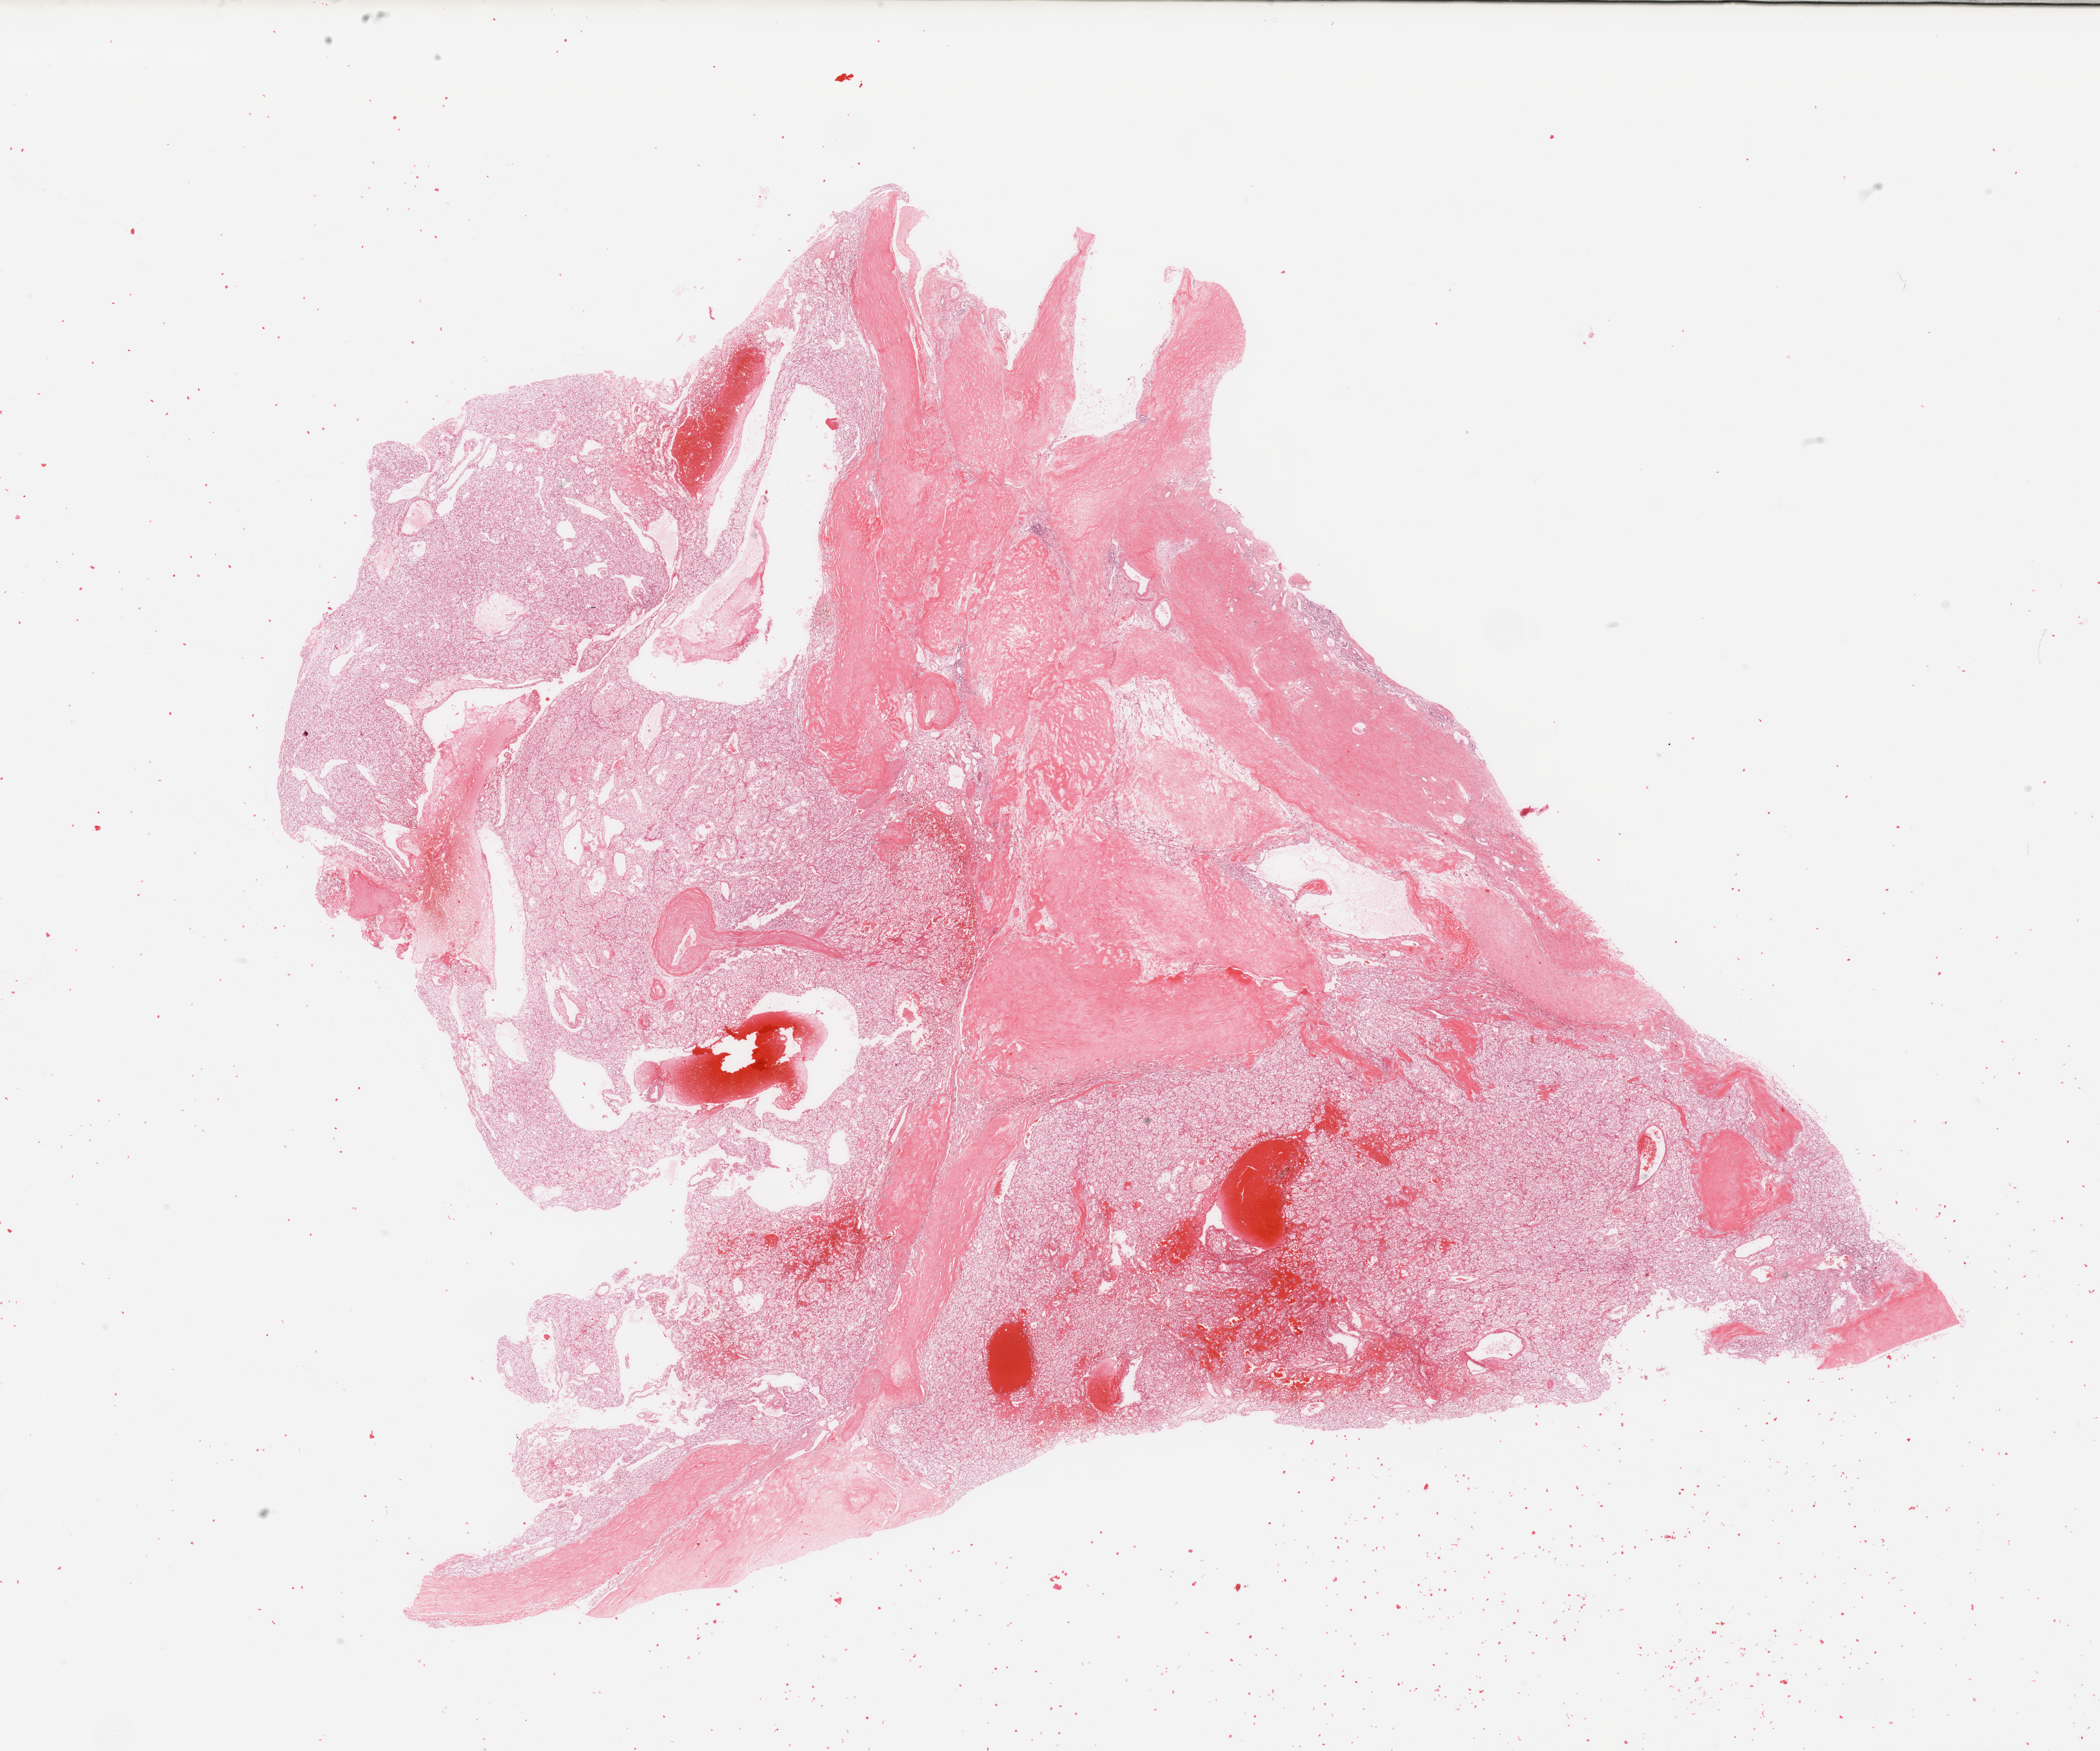
Whole-slide histology image, H&E-stained — a low-resolution overview of the entire scanned area, about 25.6 x 21.3 mm; tumour tissue sample, sampled site: kidney. 47-year-old male patient. Histologic grade: G3 (poorly differentiated). Slide review estimates, as recorded: tumour nuclei 80%, necrosis 10%.
- AJCC pathologic stage: I
- diagnosis: Renal cell carcinoma, NOS